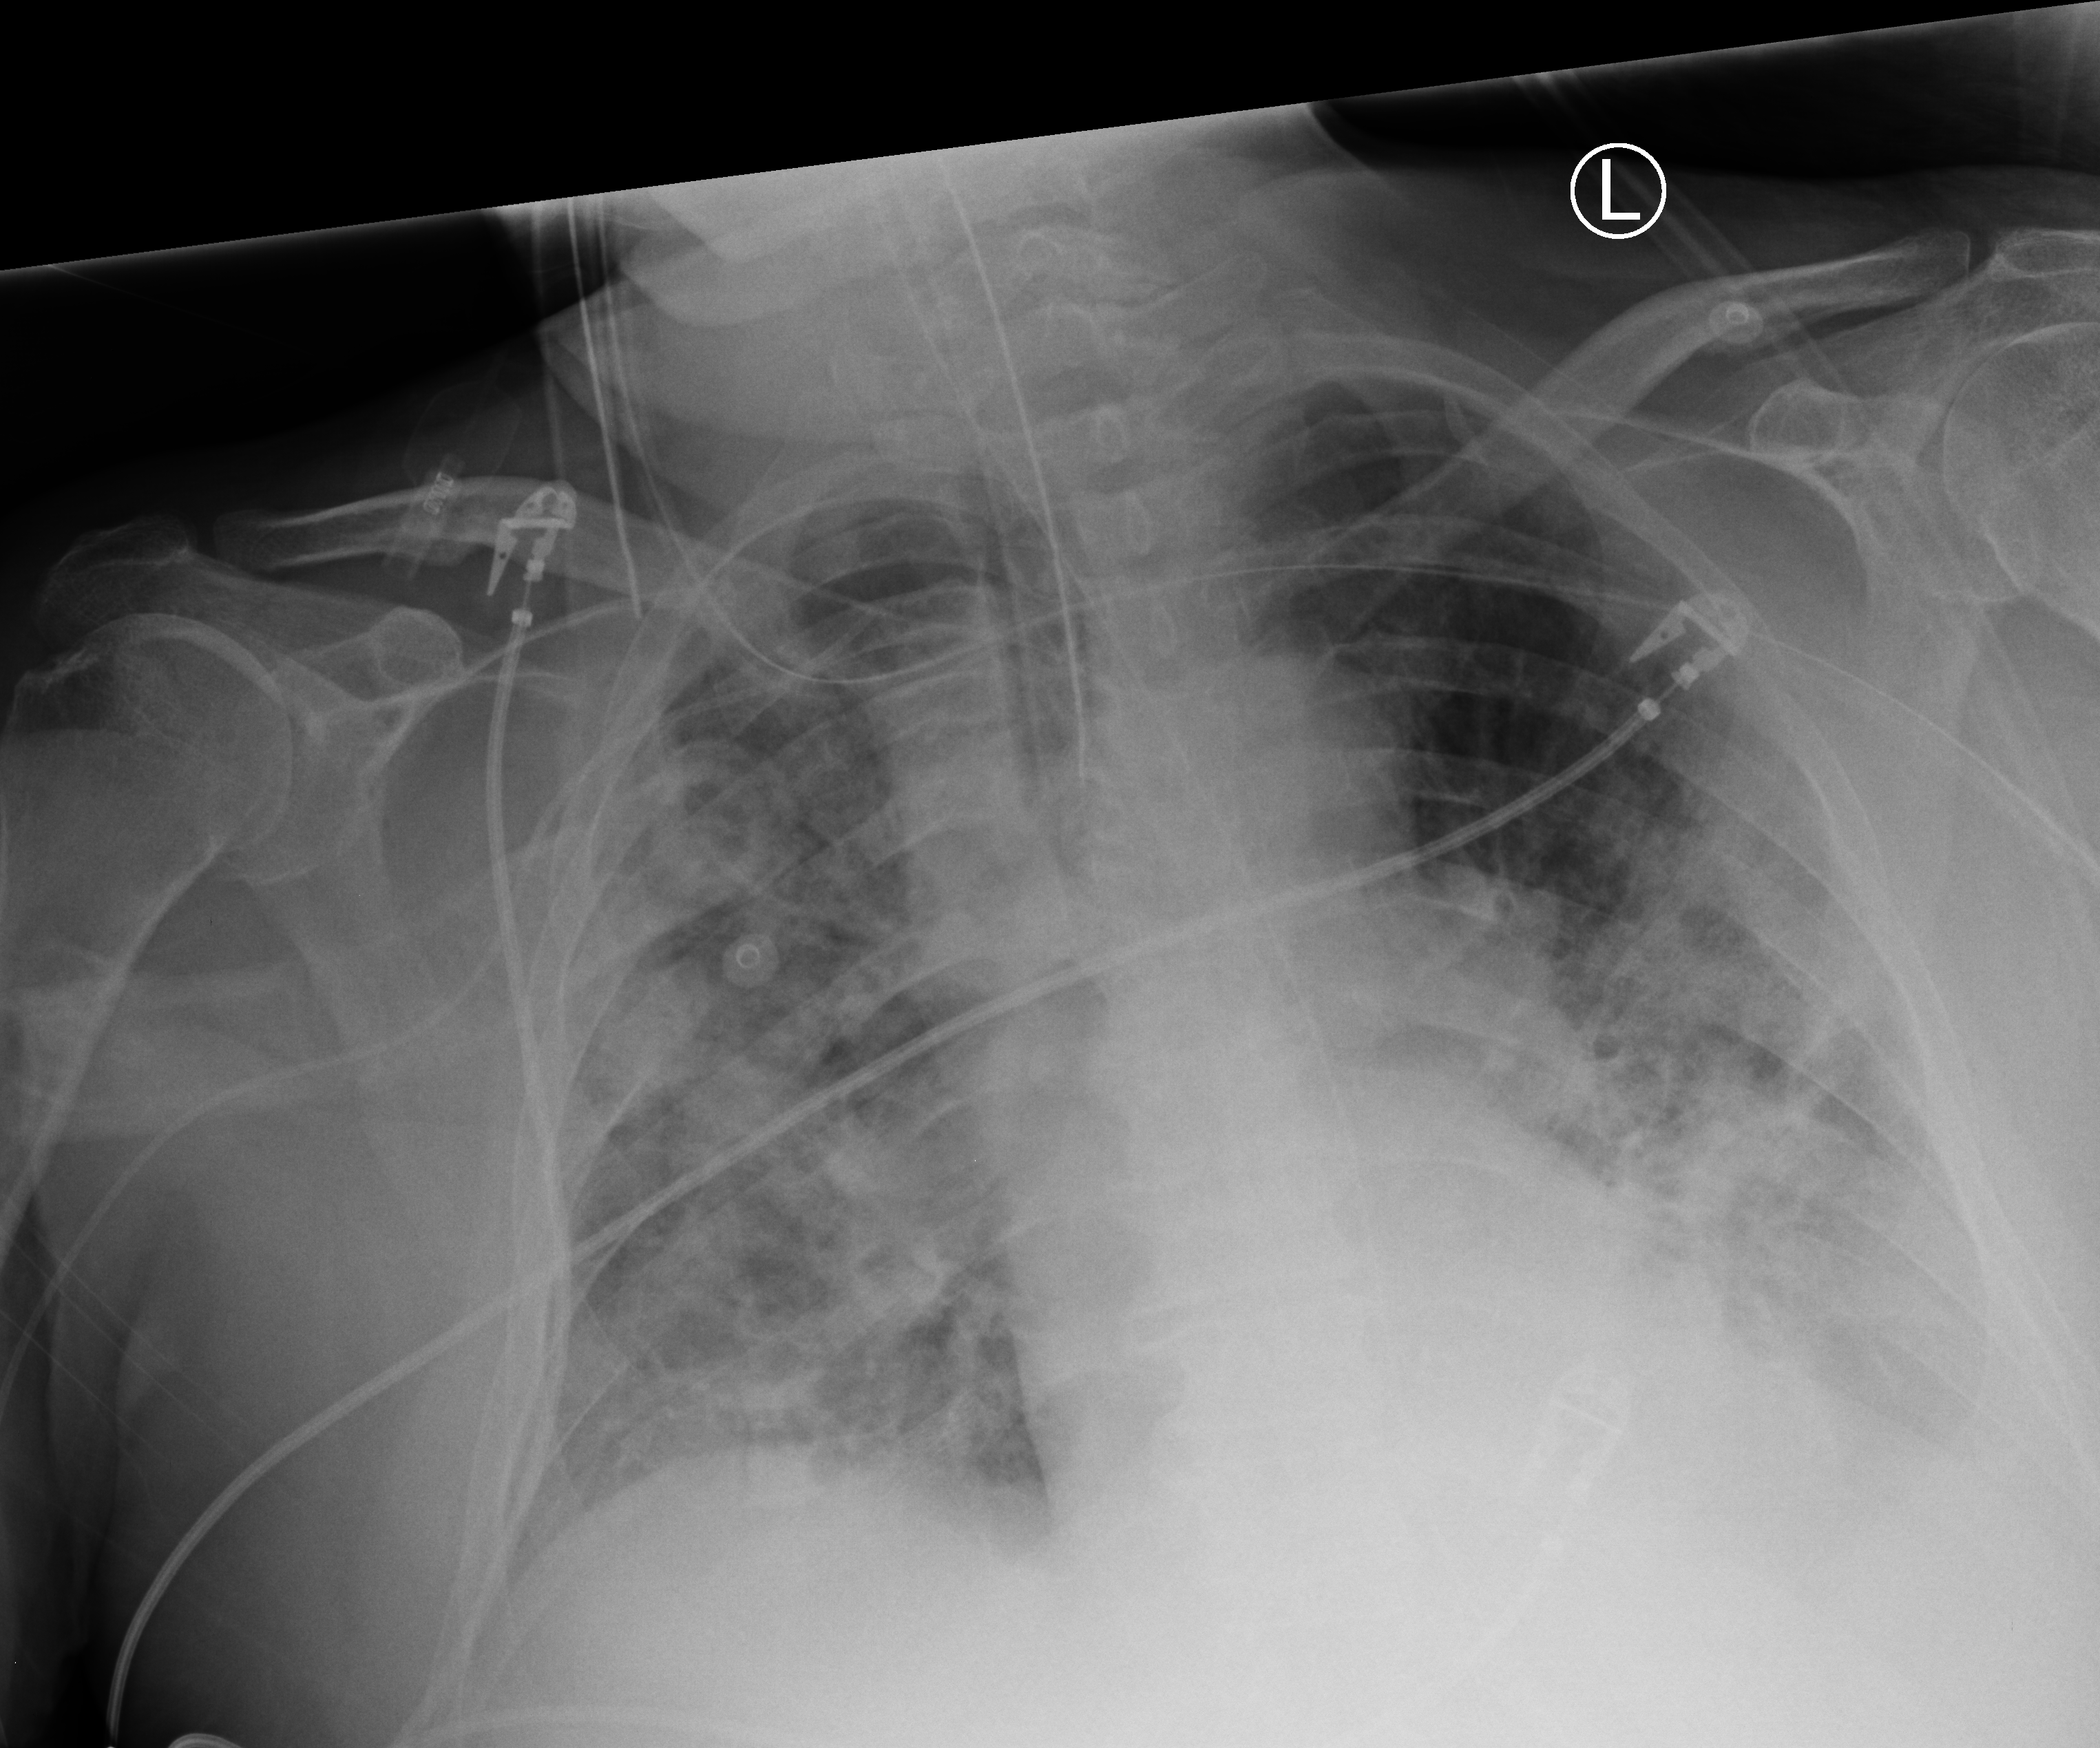
Portable chest radiograph. Patient hospitalised with COVID-19; male, aged 60–74 years.
Hospital-stay facts (about this admission, not read from this image; timing relative to this image not recorded): mechanically ventilated during this hospital stay: yes.